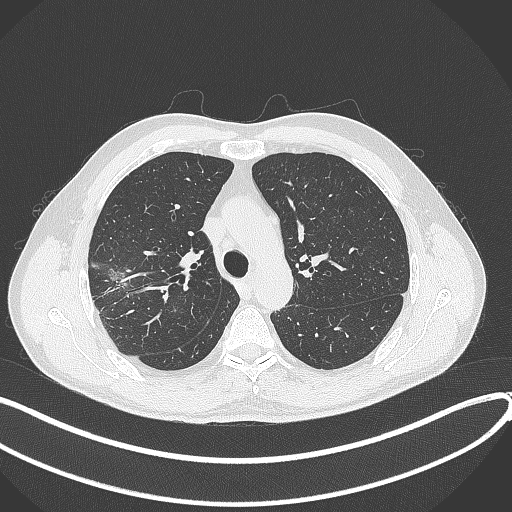
Chest CT, one axial slice; slice 296 of 381 in the series (ordered by position); reconstruction kernel B70f; lung window (W 1500 / L -600 HU); 512 × 512 image matrix, field of view 400 × 400 mm. Male patient, age 62 years. From the clinical record (not read from this slice): clinical TNM (as recorded): T1c N0 M0.
Outlined on this slice (bounding box drawn by a radiologist):
- lung tumour (recorded histology: adenocarcinoma): bounding box (x1, y1, x2, y2) in pixels: (100, 261, 133, 291)